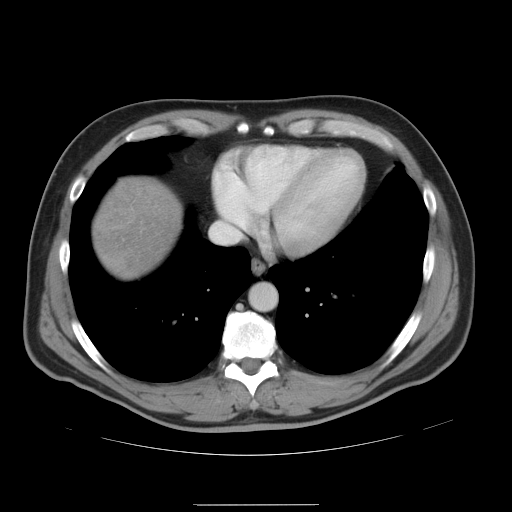
Contrast-enhanced abdominal CT, one axial slice; slice 45 of 47 in the series (ordered by position); 120 kVp; intravenous contrast given; soft-tissue window (W 400 / L 40 HU); 5 mm slice thickness; 512 × 512 image matrix, field of view 420 × 420 mm. Male patient, age 61 years. Case-level facts recorded for this patient, not image findings: diagnosis: colorectal cancer liver metastases, imaged before liver resection; multiple liver metastases: no; largest metastasis: 1.2 cm; disease in both lobes: no.
Annotated regions visible in this slice (manually delineated by an expert):
- liver: box from (x=94, y=176) to (x=184, y=279) px
- planned liver remnant (the part of the liver to remain after resection): (x=94, y=177)–(x=184, y=279)